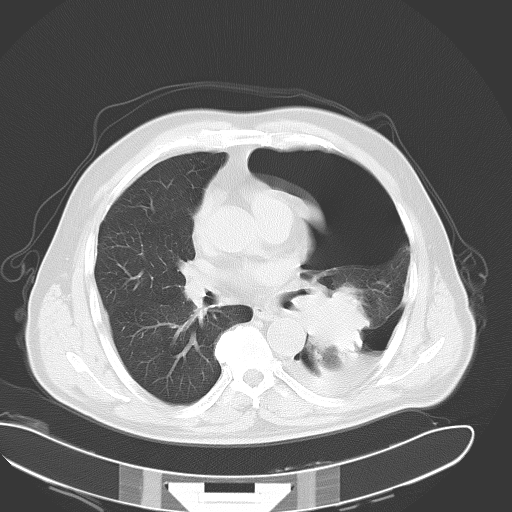
Chest CT, one axial slice. Position 24 of 43 along the scan axis. Reconstruction kernel B70f. 120 kVp. Lung window (W 1500 / L -600 HU). 8 mm slice thickness. 512 × 512 image matrix, field of view 418 × 418 mm. Male patient, age 62 years. From the clinical record (not read from this slice): clinical TNM (as recorded): T3 N0 M1.
Outlined on this slice (rectangle marked by the reading radiologist):
- lung tumour (recorded histology: adenocarcinoma): bounding box (x1, y1, x2, y2) in pixels: (293, 282, 369, 350)
- lung tumour (recorded histology: adenocarcinoma): (301, 280, 372, 361)